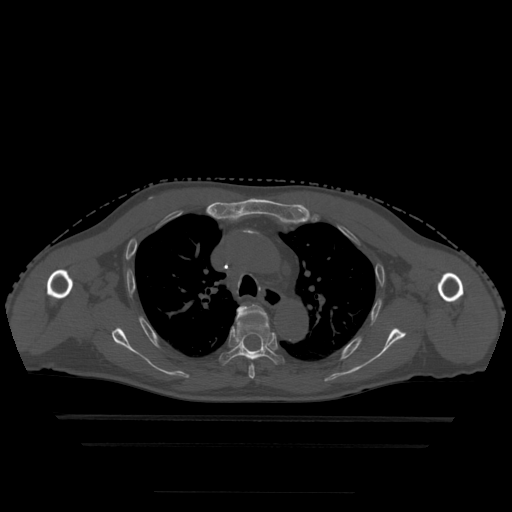
CT including the spine, one axial slice. Position 342 of 522 along the scan axis. Bone window (W 1800 / L 400 HU). 1.25 mm slice thickness. 512 × 512 image matrix. Patient age 68 years. Case-level facts recorded for this patient, not image findings: primary cancer: urothelial.
Annotated regions visible in this slice (semi-automatically segmented with operator editing):
- T4 vertebra: bounding box [x1, y1, x2, y2] px = [237, 304, 269, 379]
- T5 vertebra: [220, 316, 284, 365]